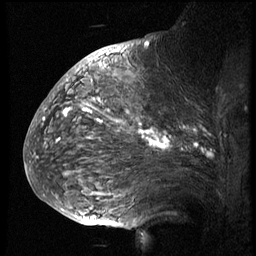
Breast MRI (dynamic contrast-enhanced), one sagittal slice; slice 42 of 74 in the series (ordered by position); 3 images stored at this slice position (order not interpretable as contrast timing); 1.5 T; TE 4.2 ms, TR 8.9 ms; 256 × 256 image matrix, field of view 200 × 200 mm. Patient: female, 57 years. From the clinical record (not read from this slice): setting: breast cancer imaged before/during neoadjuvant chemotherapy; receptor status: HER2-positive.
Annotated regions visible in this slice (semi-automatic segmentation, software-assisted and operator-edited):
- analysis volume of interest (the breast-tissue region the enhancement analysis was run in; not a lesion): bounding box (x1, y1, x2, y2) in pixels: (51, 67, 248, 173)
- tumour enhancement mask (voxels above the 140 % enhancement threshold inside the analysis volume of interest): (58, 100, 211, 156)